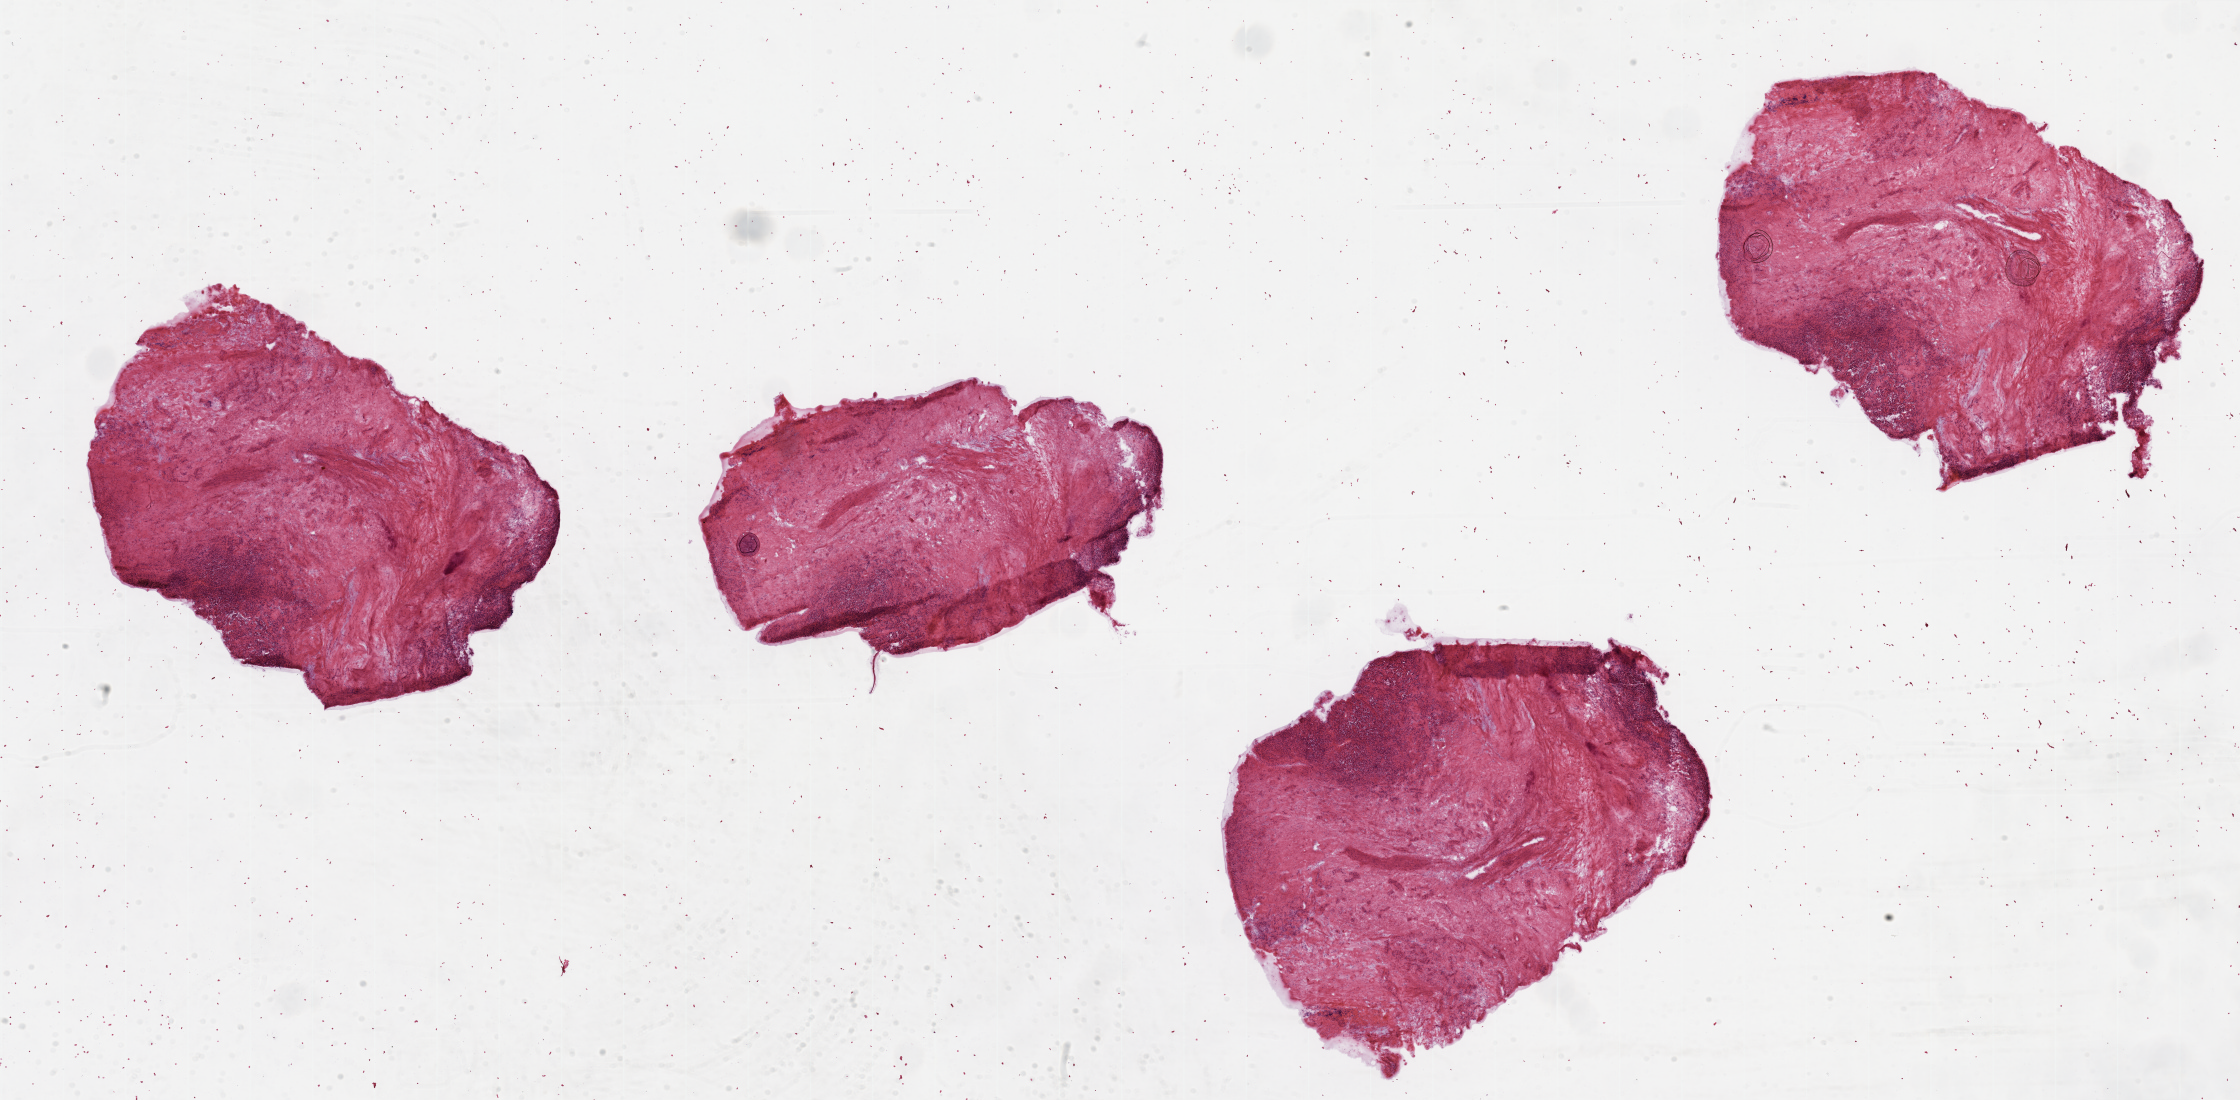
Digitized Hematoxylin and eosin (H&E) stained tissue section (whole slide) — a low-resolution overview of the entire scanned area, about 35.4 x 17.4 mm (slide scanned at 20x); tumour tissue sample, sampled site: kidney. Patient: male, age 78 years. Histologic grade: G2 (moderately differentiated). Slide review estimates, as recorded: tumour nuclei 30%, necrosis 30%.
AJCC pathologic stage: I. Primary tumour site (as recorded): upper pole. Diagnosis: Renal cell carcinoma, NOS.